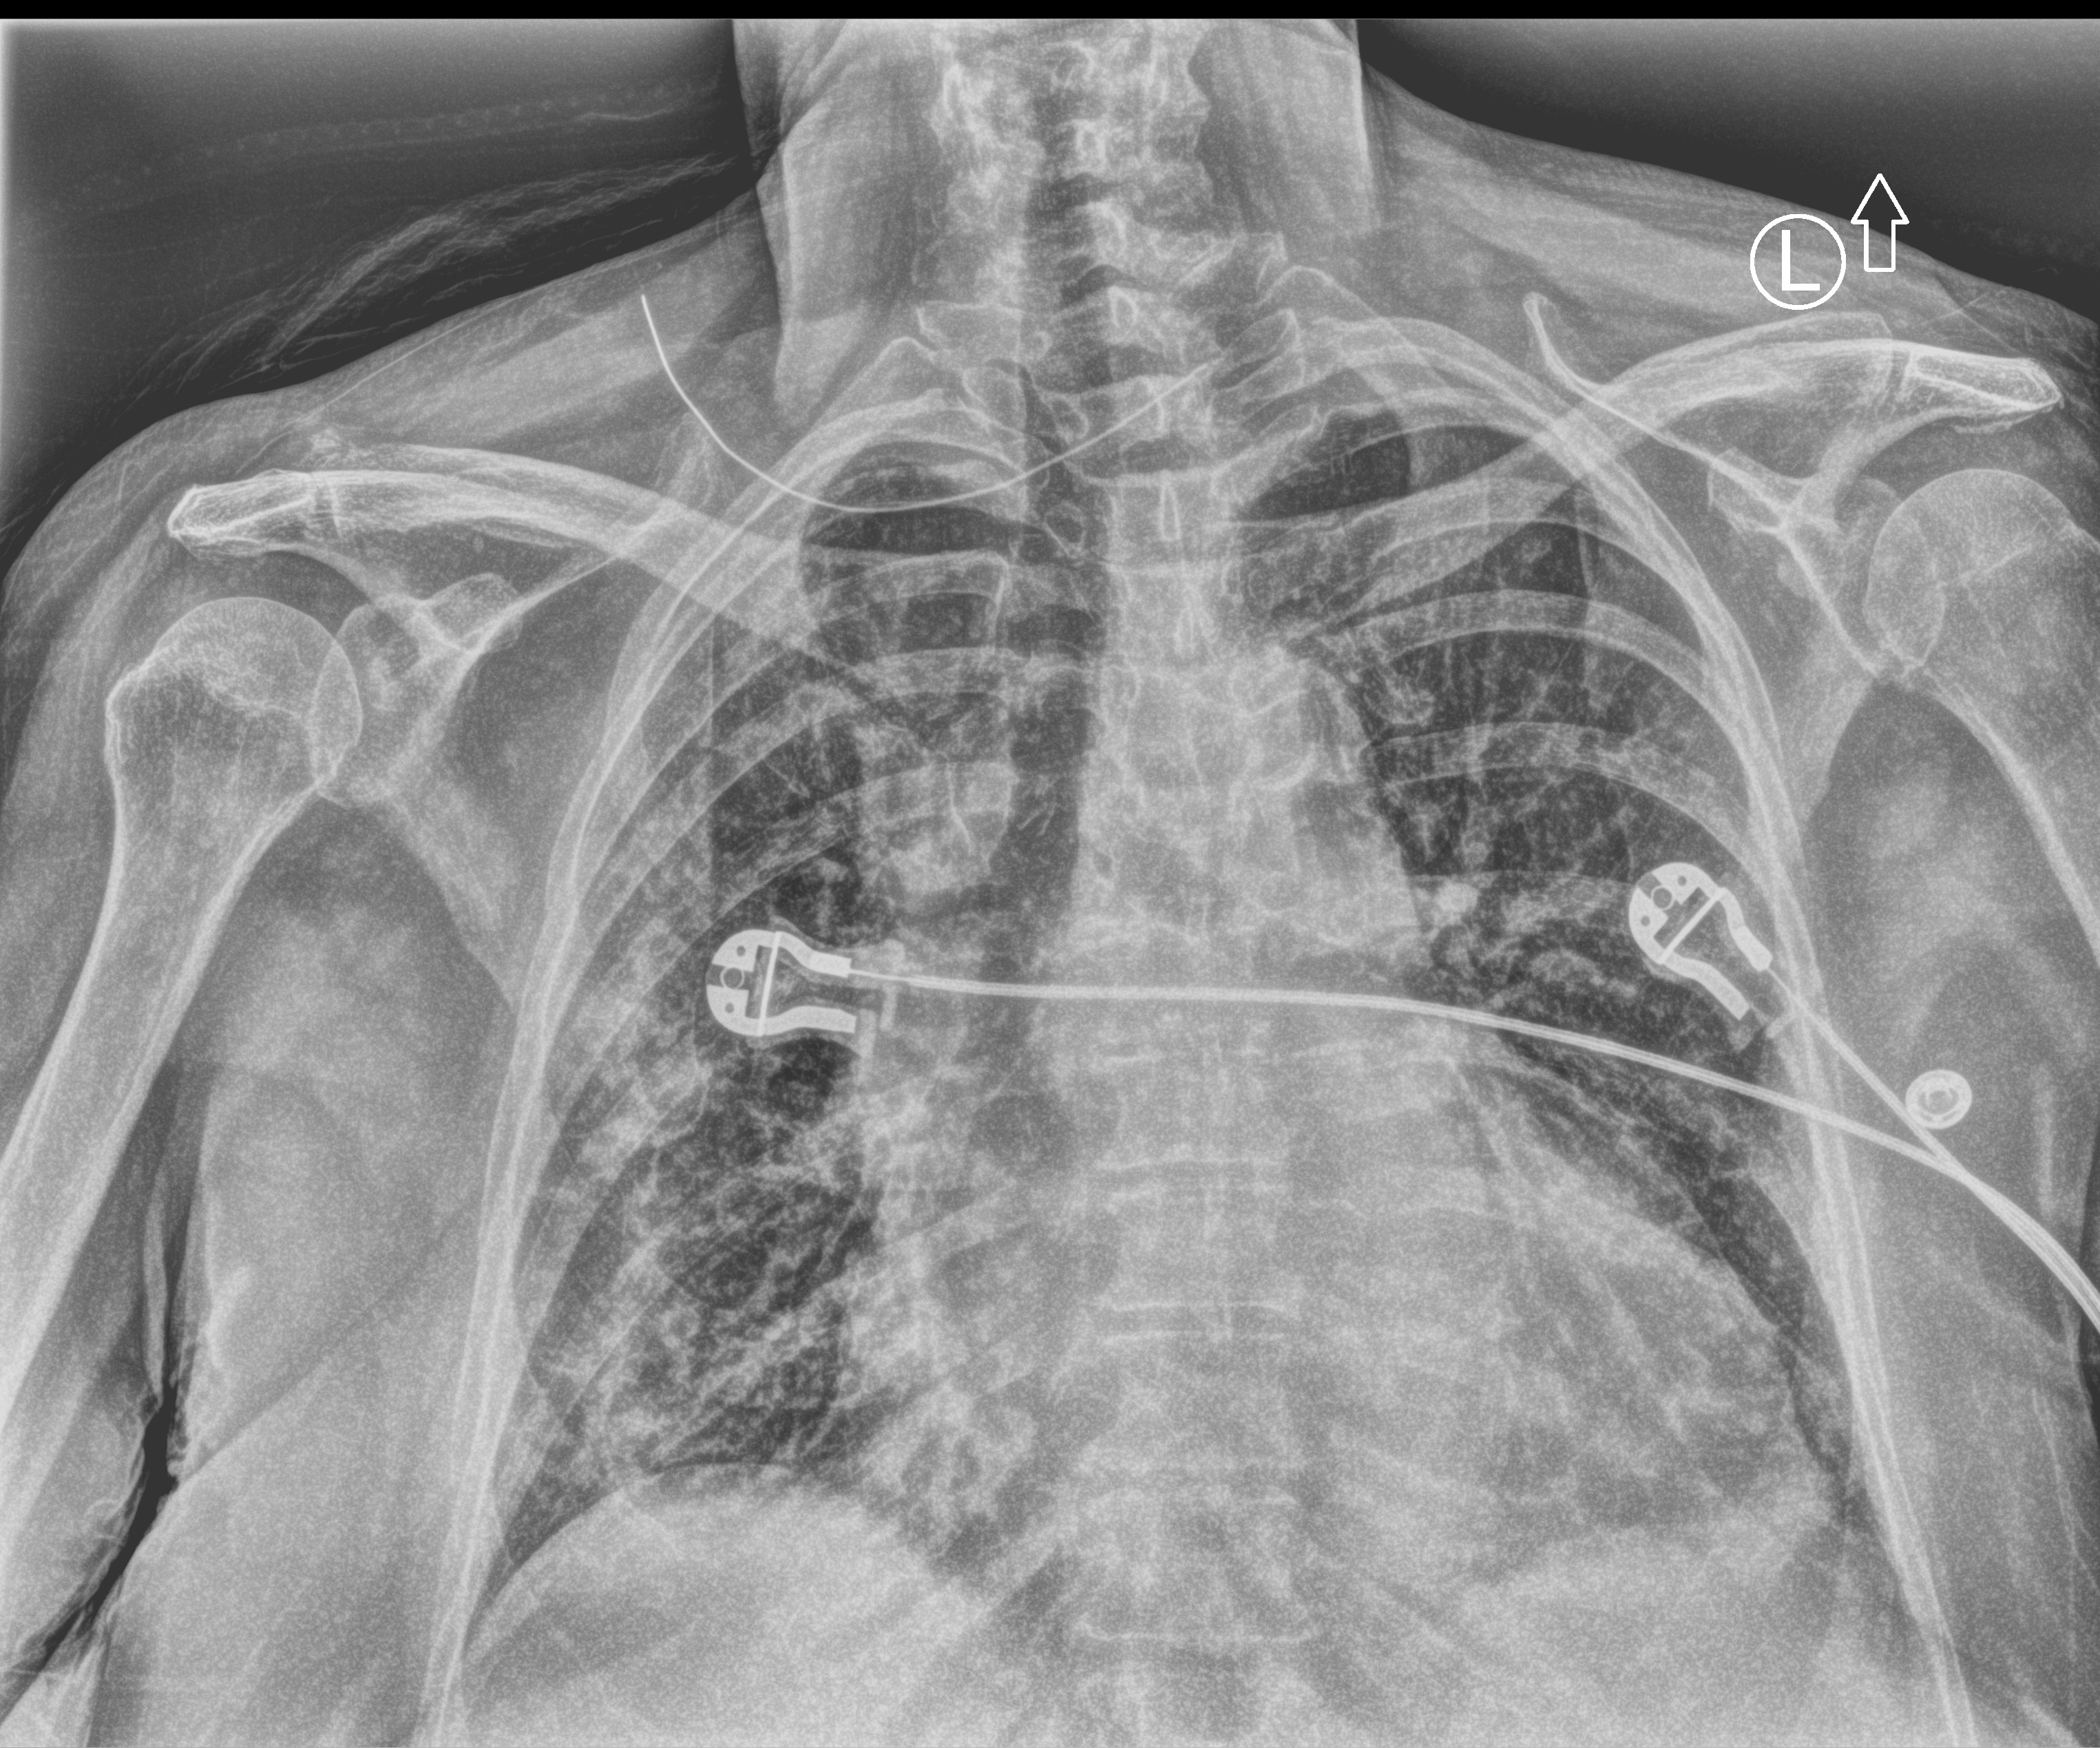
Chest X-ray (portable). Patient hospitalised with COVID-19; female, aged 75–90 years.
From the hospital-stay record, not from the radiograph (when in the stay this image was taken is not recorded): chronic kidney disease (admission record): no; admitted to intensive care during this hospital stay: no.